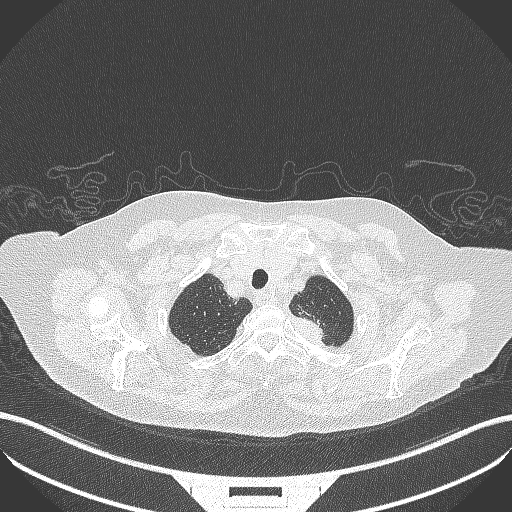
Chest CT, one axial slice; slice 310 of 353 in the series (ordered by position); reconstruction kernel B70f; lung window (W 1500 / L -600 HU); 512 × 512 image matrix, field of view 400 × 400 mm. Patient: female, 81 years. From the clinical record (not read from this slice): clinical TNM (as recorded): T2a N0 M0.
Structures marked on this image (bounding box drawn by a radiologist):
- lung tumour (recorded histology: adenocarcinoma): box from (x=295, y=313) to (x=338, y=353) px